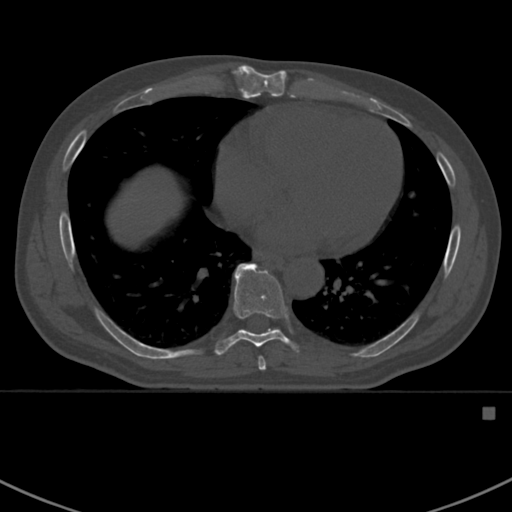
CT including the spine, one axial slice. Position 399 of 412 along the scan axis. Reconstruction kernel Br40s. Bone window (W 1800 / L 400 HU). 512 × 512 image matrix, field of view 358 × 358 mm. Male patient, age 59 years. Case-level facts recorded for this patient, not image findings: primary cancer: prostate.
Outlined on this slice (semi-automatically segmented with operator editing):
- T7 vertebra: box from (x=258, y=357) to (x=266, y=371) px
- T8 vertebra: (x=215, y=263)–(x=299, y=355)
- T9 vertebra: (x=236, y=265)–(x=279, y=330)